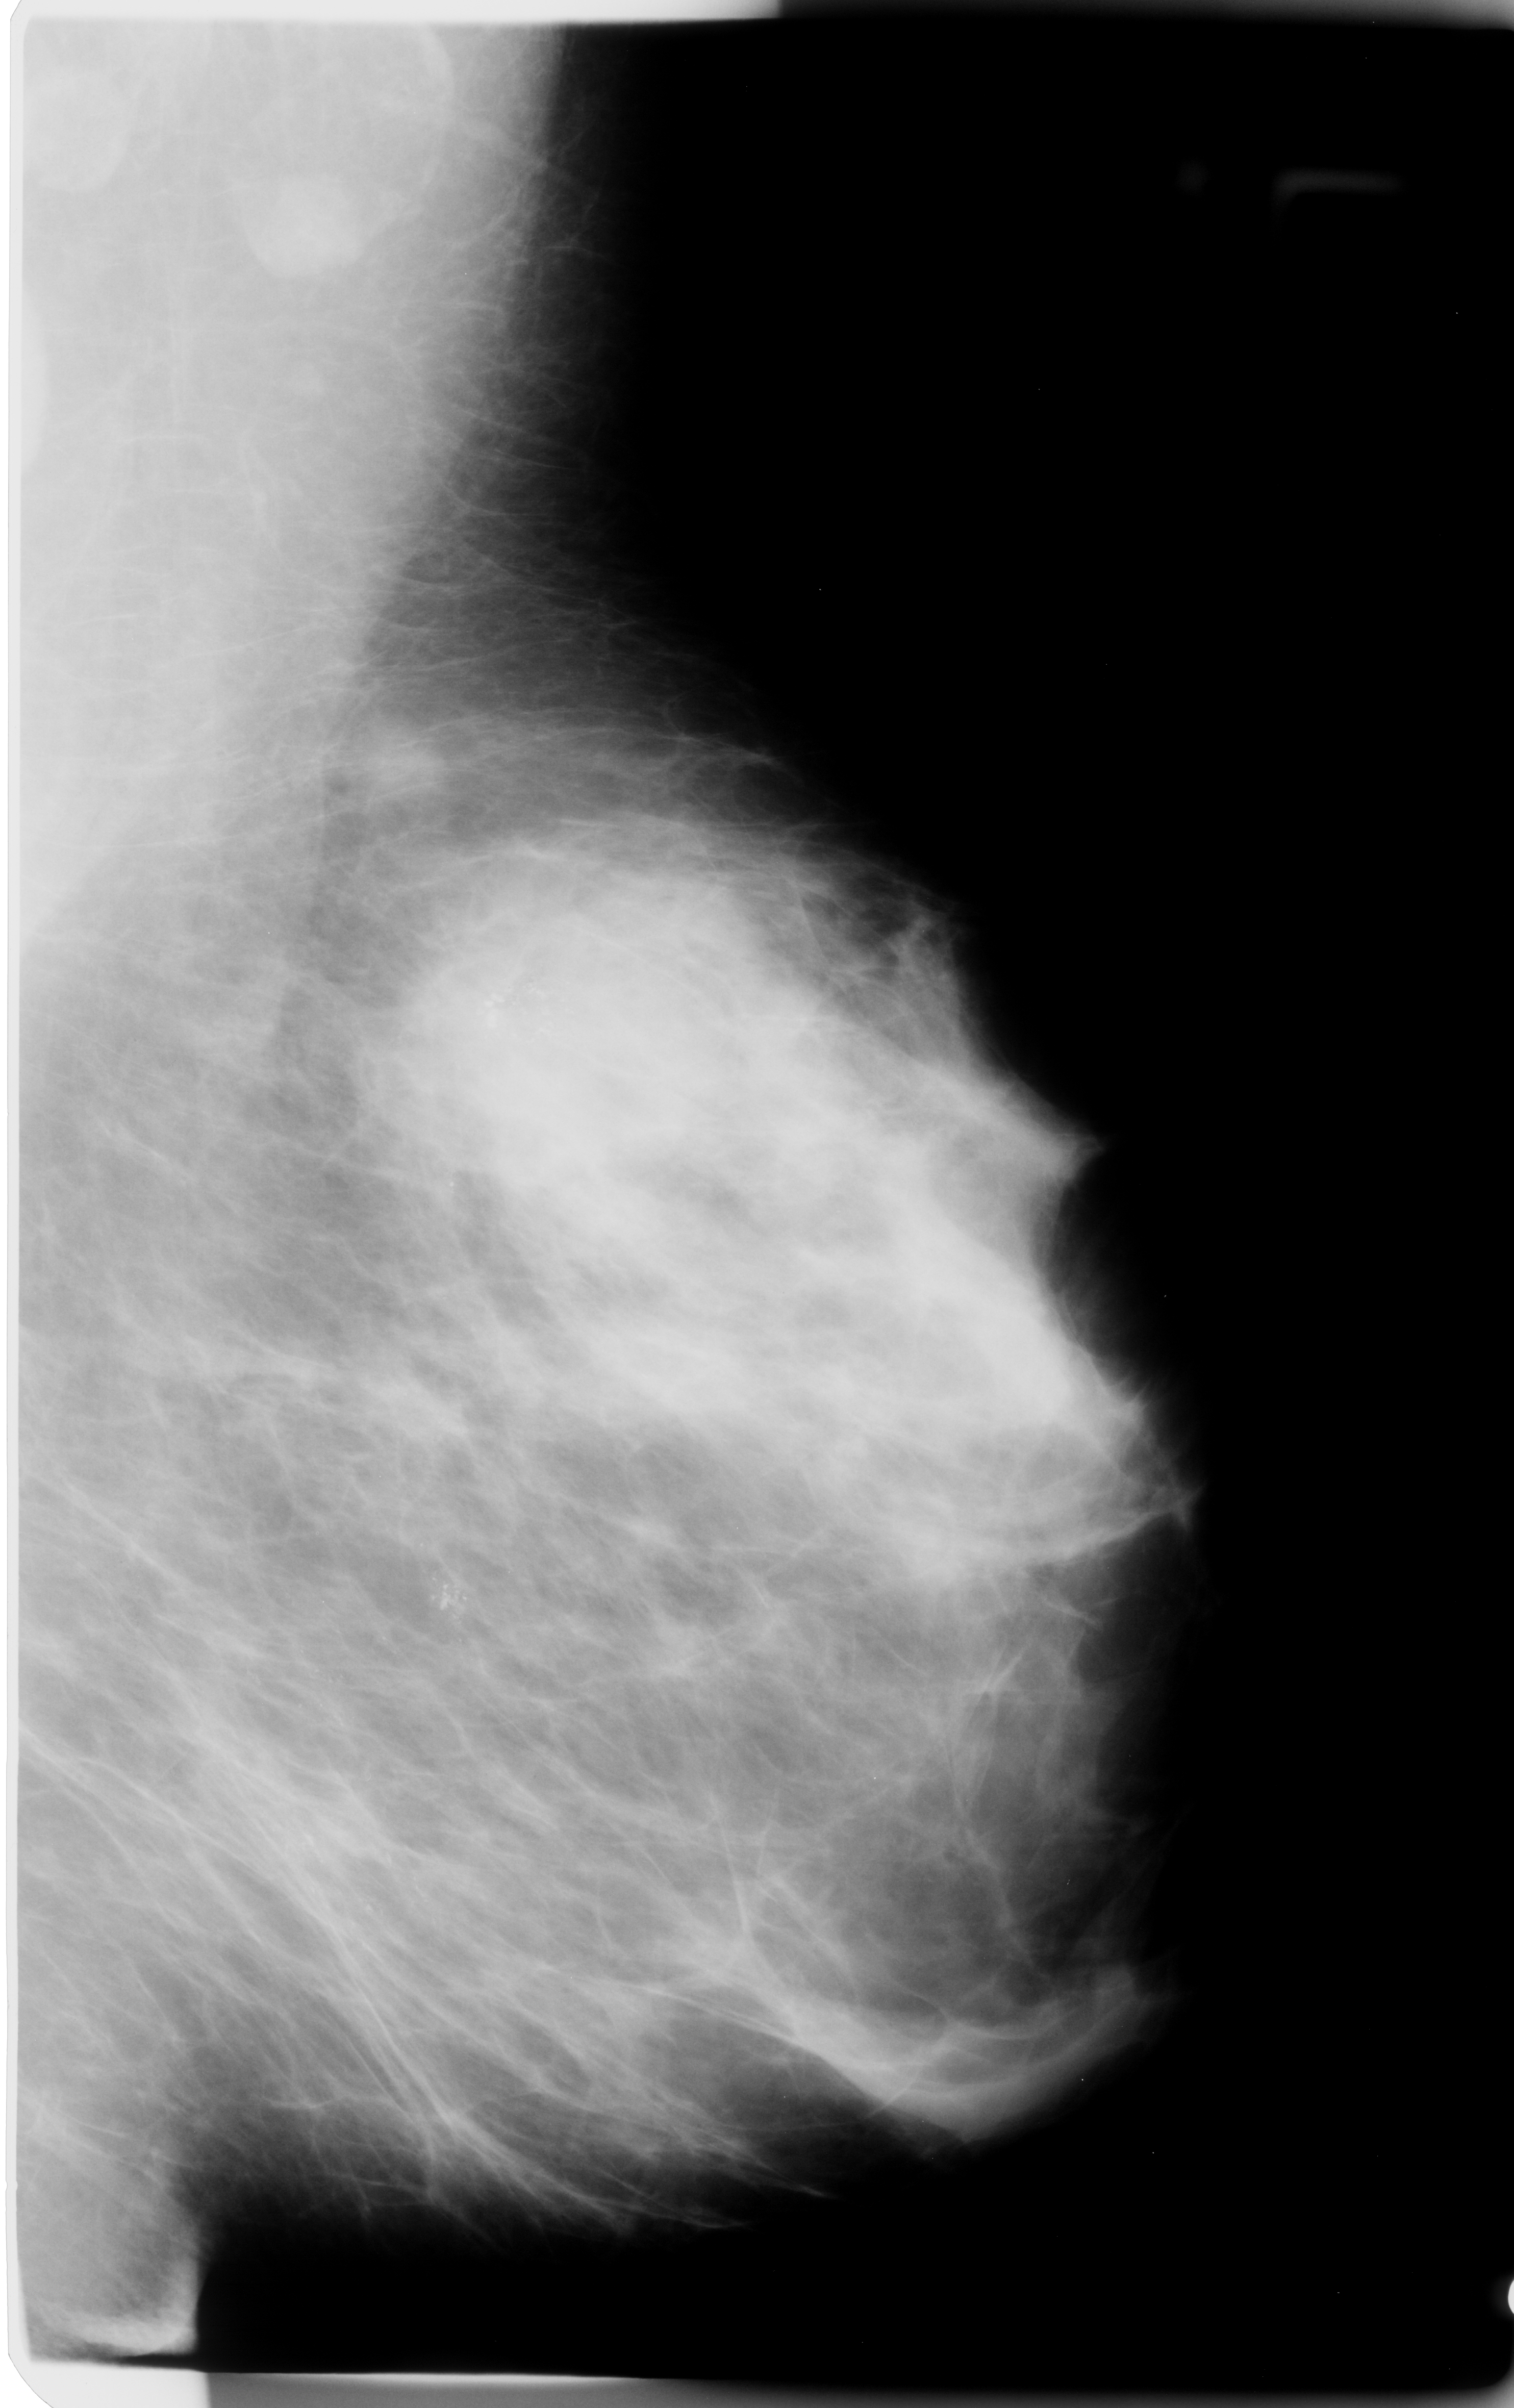
Mammogram (digitized film). Left breast. MLO view. Breast composition: scattered fibroglandular densities (BI-RADS density category 2 of 4). 1514 × 2408 image matrix.
Marked abnormalities (boxes around the expert regions of interest):
- Finding 1 of 2: calcifications, morphology pleomorphic / fine linear branching, distribution regional; BI-RADS assessment category 5; pathology result (as recorded, not read from the image): malignant: bounding box (x1, y1, x2, y2) in pixels: (318, 861, 780, 1246)
- Finding 2 of 2: calcifications, morphology pleomorphic / fine linear branching, distribution regional; BI-RADS assessment category 5; pathology result (as recorded, not read from the image): malignant: (399, 1546, 483, 1646)